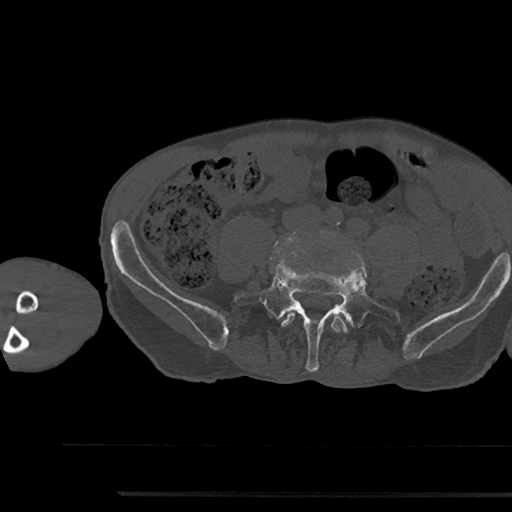
CT including the spine, one axial slice. Slice 365 of 797 in the series (ordered by position). 120 kVp. Bone window (W 1800 / L 400 HU). 512 × 512 image matrix, field of view 367 × 367 mm. Male patient, age 79 years. From the clinical record (not read from this slice): primary cancer: prostate.
Outlined on this slice (semi-automatic segmentation, software-assisted and operator-edited):
- L4 vertebra: box from (x=281, y=311) to (x=348, y=333) px
- L5 vertebra: (x=234, y=262)–(x=400, y=372)